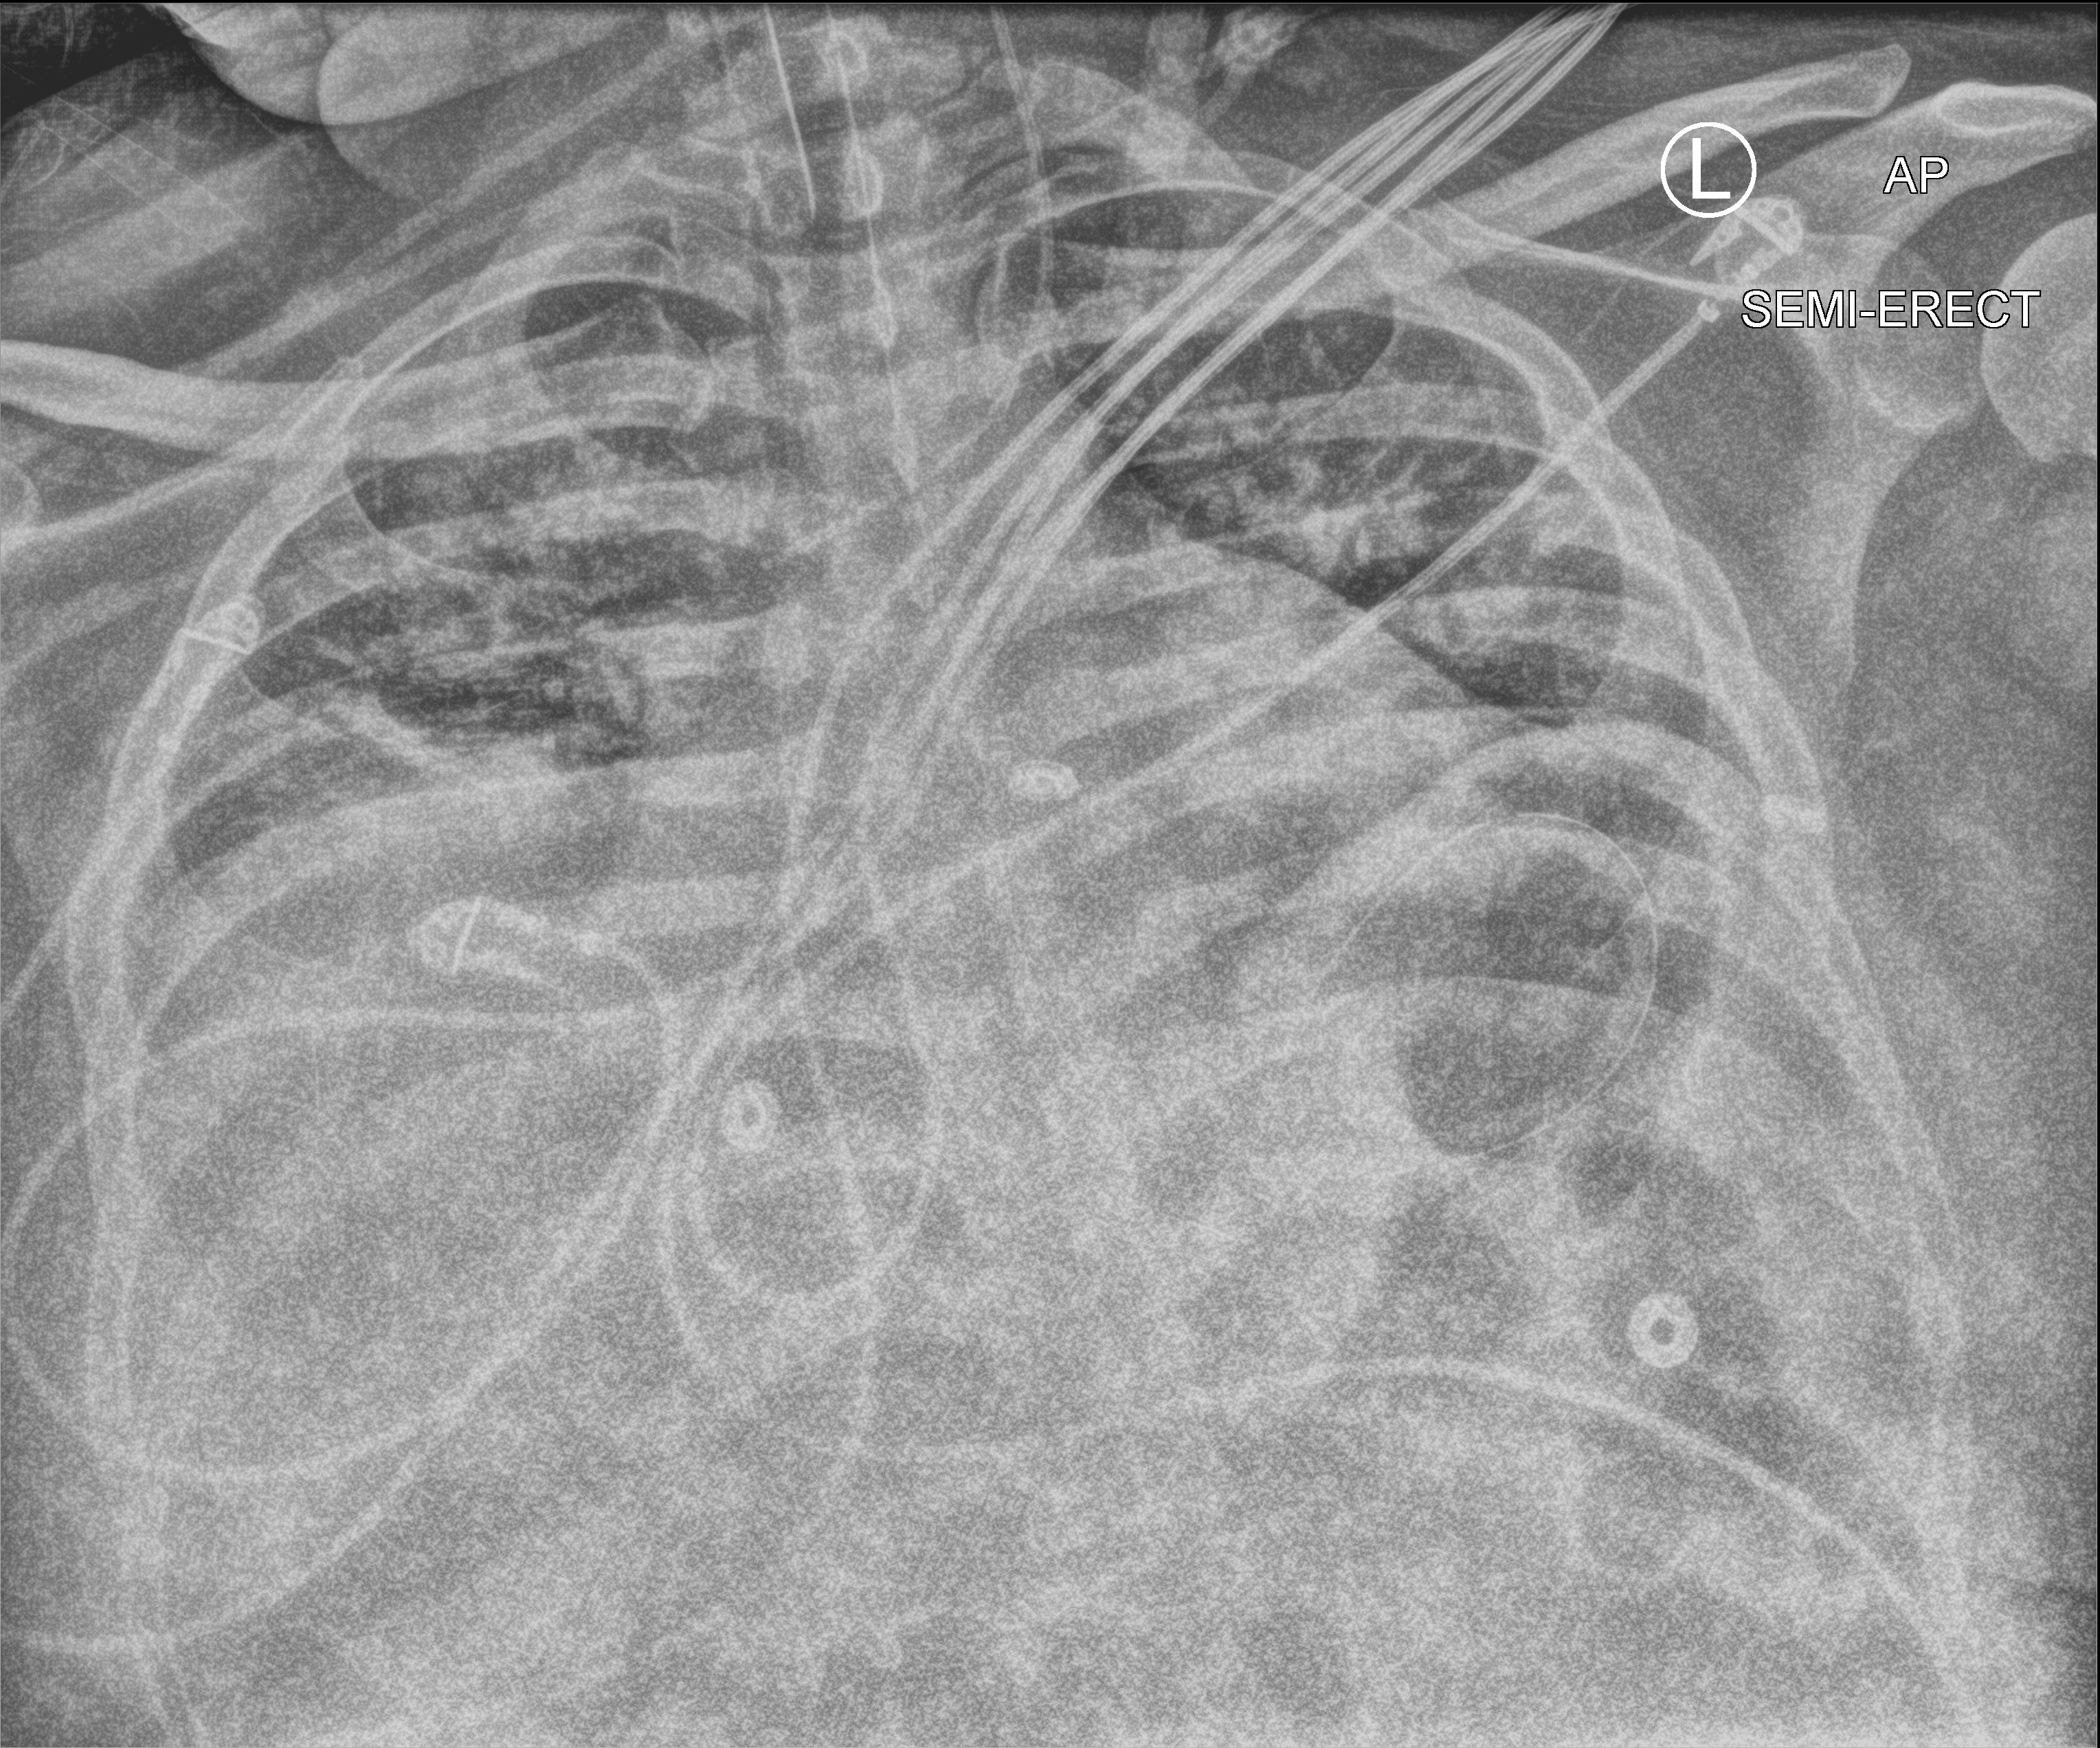
Bedside chest radiograph (computed radiography); anteroposterior (AP) projection. Patient hospitalised with COVID-19; male, aged 18–59 years.
Hospital-stay facts (about this admission, not read from this image; timing relative to this image not recorded): admitted to intensive care during this hospital stay: yes.